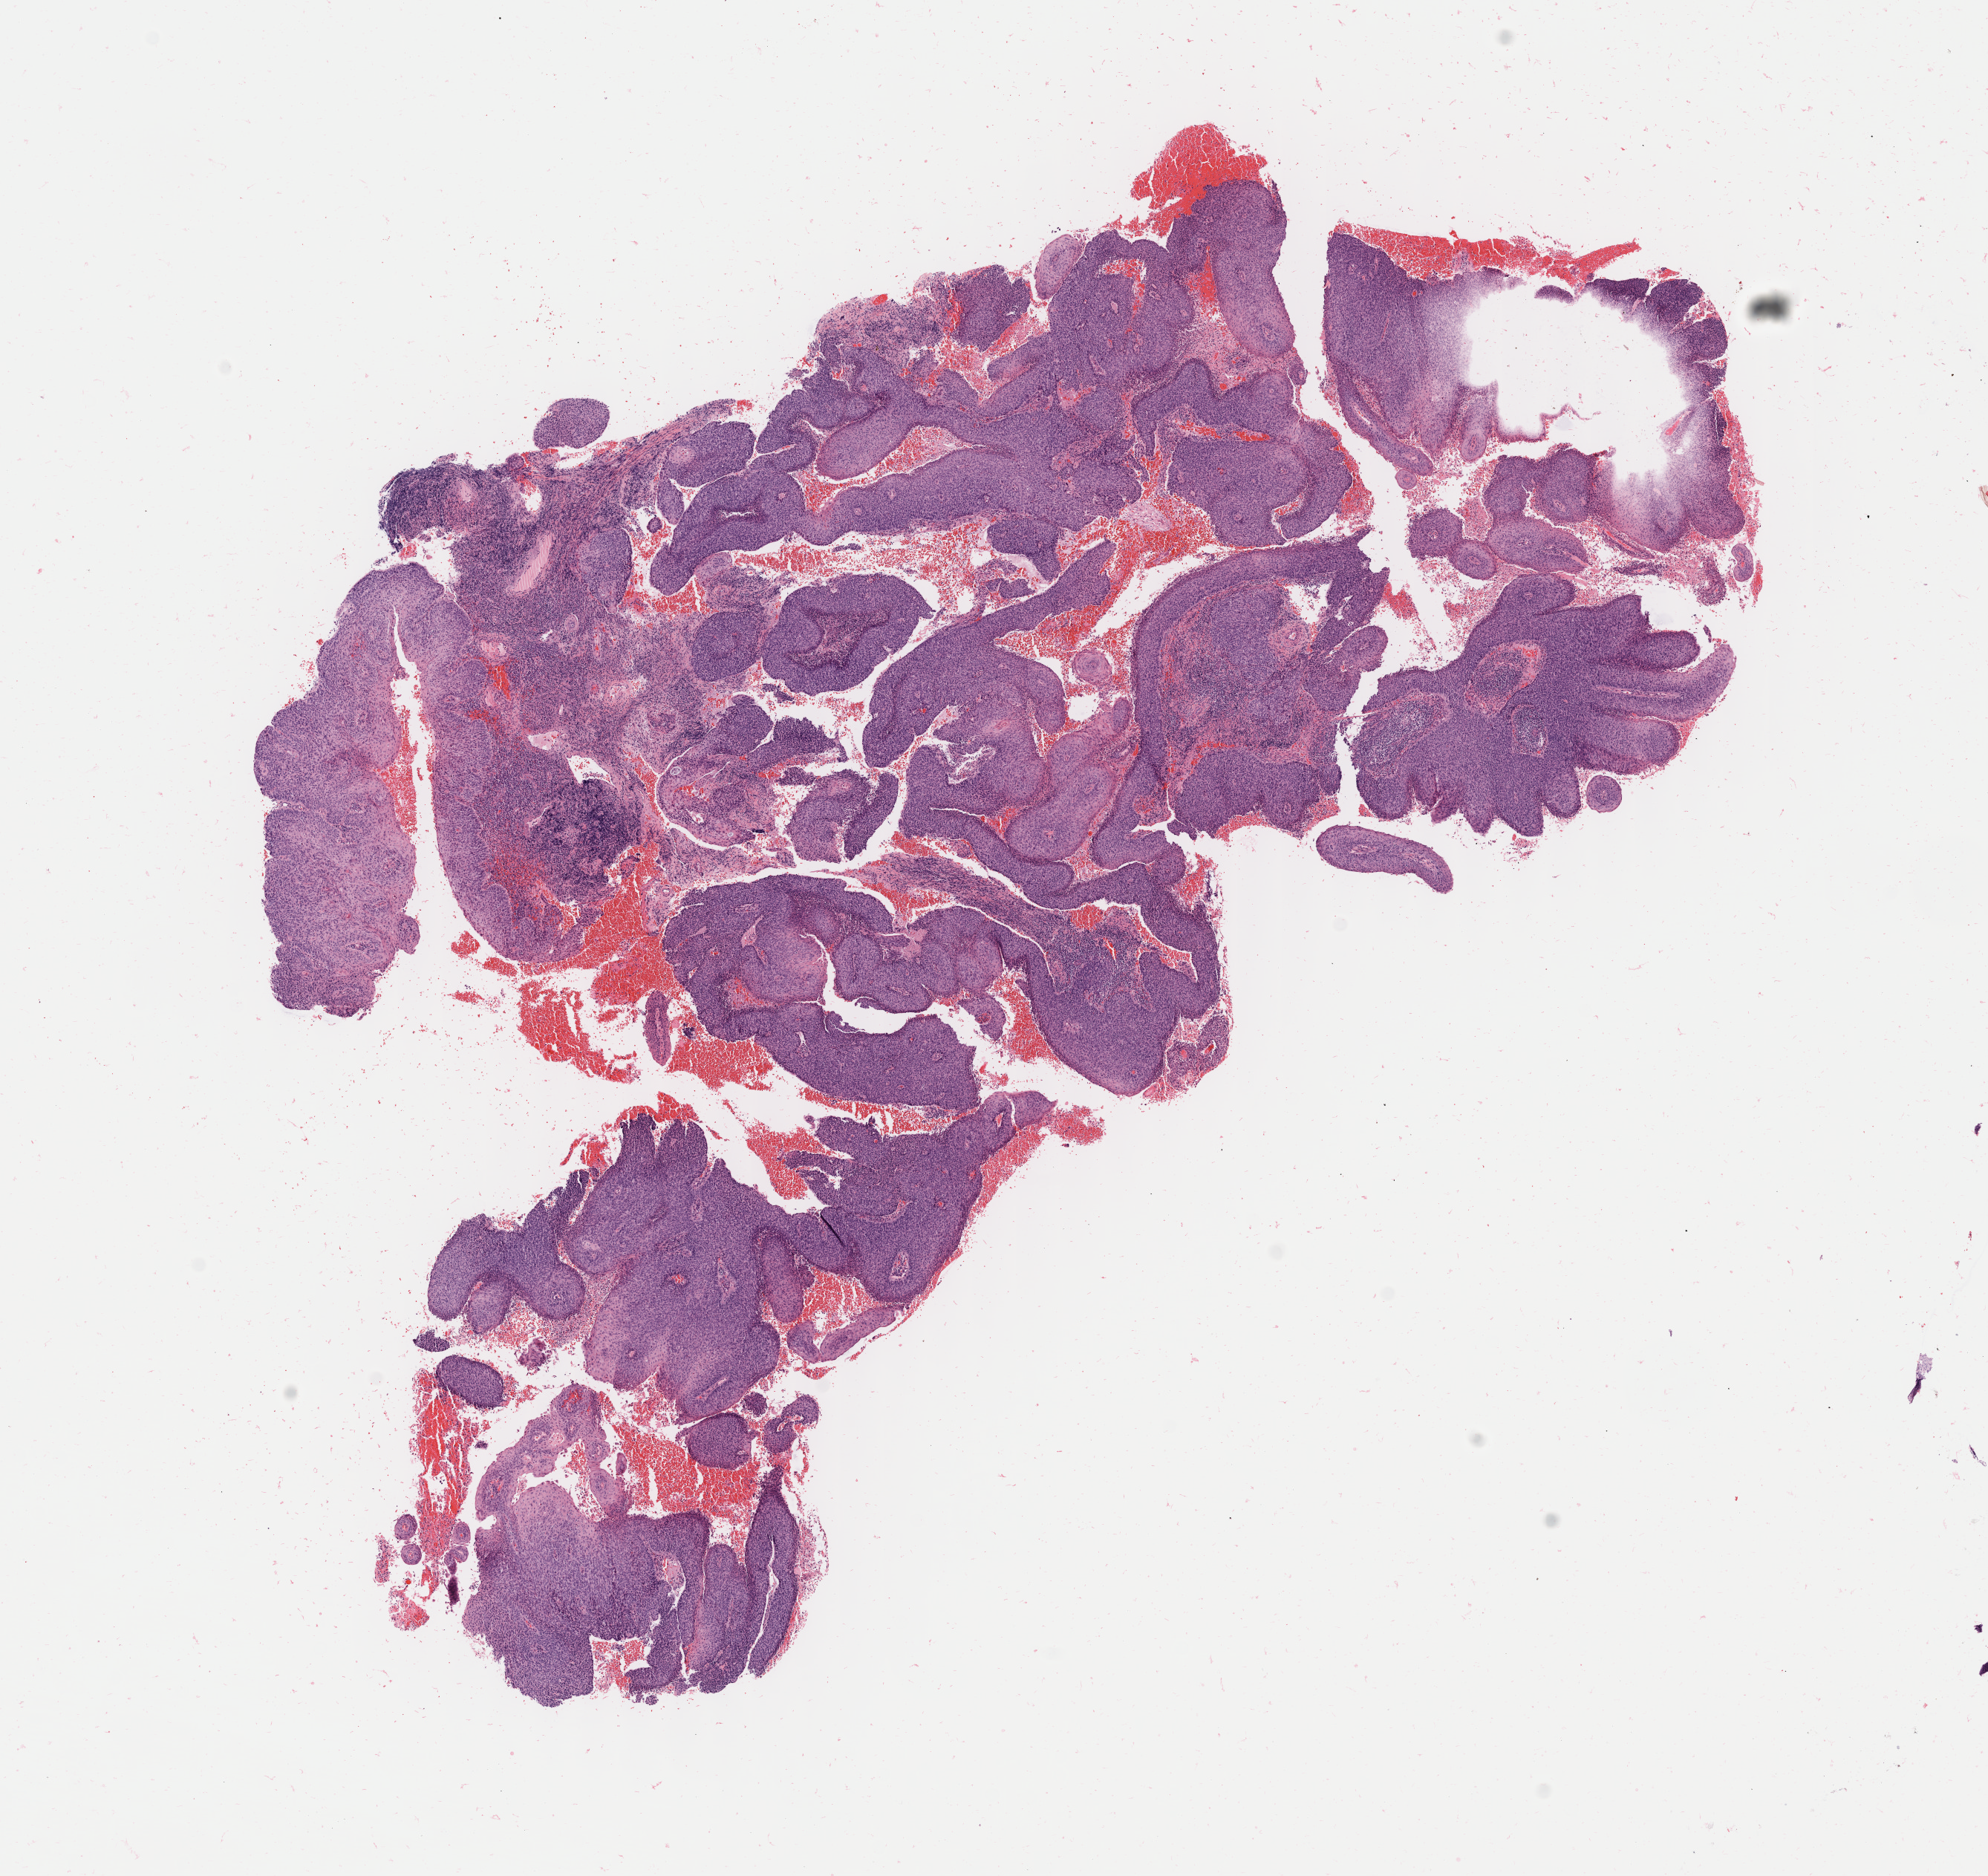
Haematoxylin and eosin whole-slide image, whole scanned area (about 10.7 x 10.0 mm) shown as a low-resolution overview. Specimen: tumor tissue. Anatomic site: cervix. Patient: female, 54 years old.
Histologic diagnosis: Squamous cell carcinoma, large cell, nonkeratinizing, NOS.